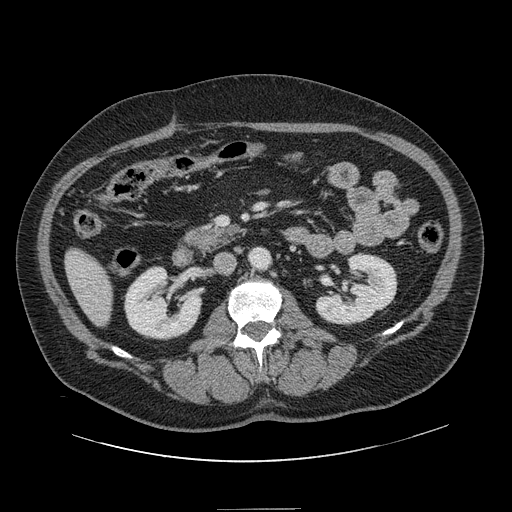
Contrast-enhanced abdominal CT, one axial slice; position 42 of 154 along the scan axis; intravenous contrast given; soft-tissue window (W 400 / L 40 HU); 2.5 mm slice thickness; 512 × 512 image matrix, field of view 451 × 451 mm. Male patient, age 61 years. From the clinical record (not read from this slice): diagnosis: colorectal cancer liver metastases, imaged before liver resection; multiple liver metastases: yes; largest metastasis: 2.6 cm.
Annotated regions visible in this slice (expert manual segmentation):
- liver: bounding box (x1, y1, x2, y2) in pixels: (66, 250, 112, 325)
- planned liver remnant (the part of the liver to remain after resection): (66, 250, 112, 325)